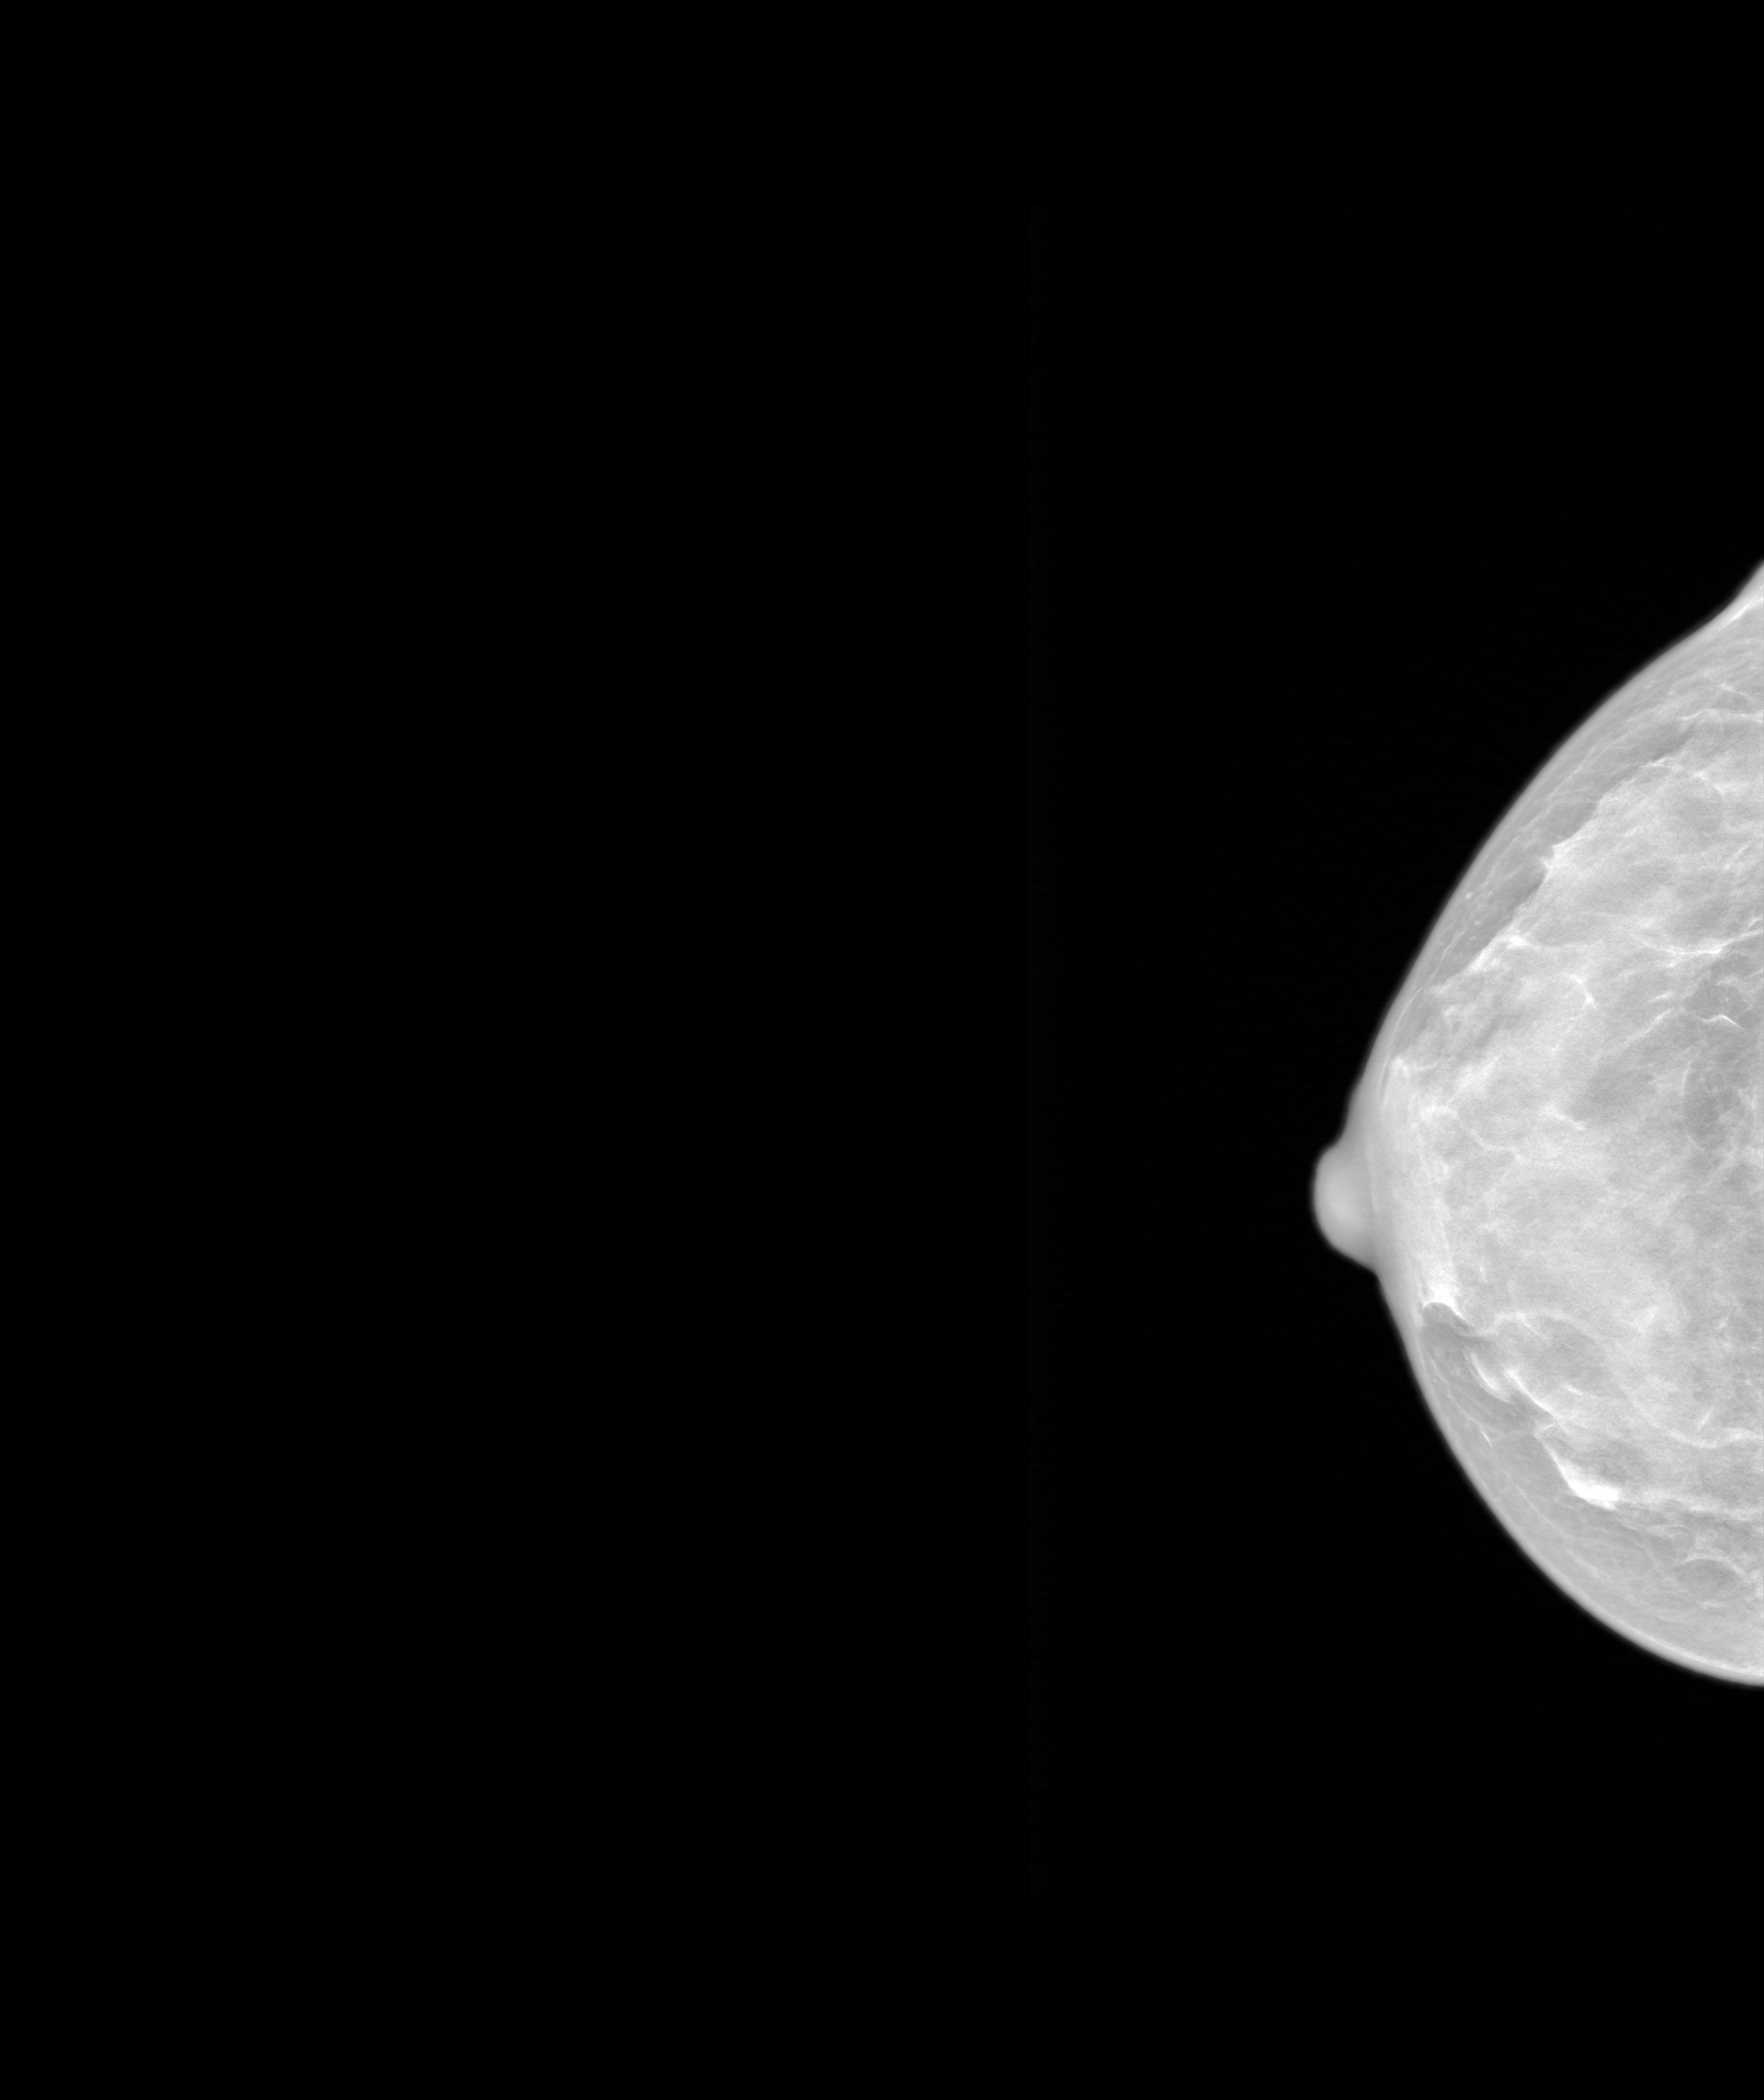
Annual screening mammography examination. Patient aged 47 years (female).
Image type: synthesized 2-D view from tomosynthesis. Breast: right. Projection: CC view.